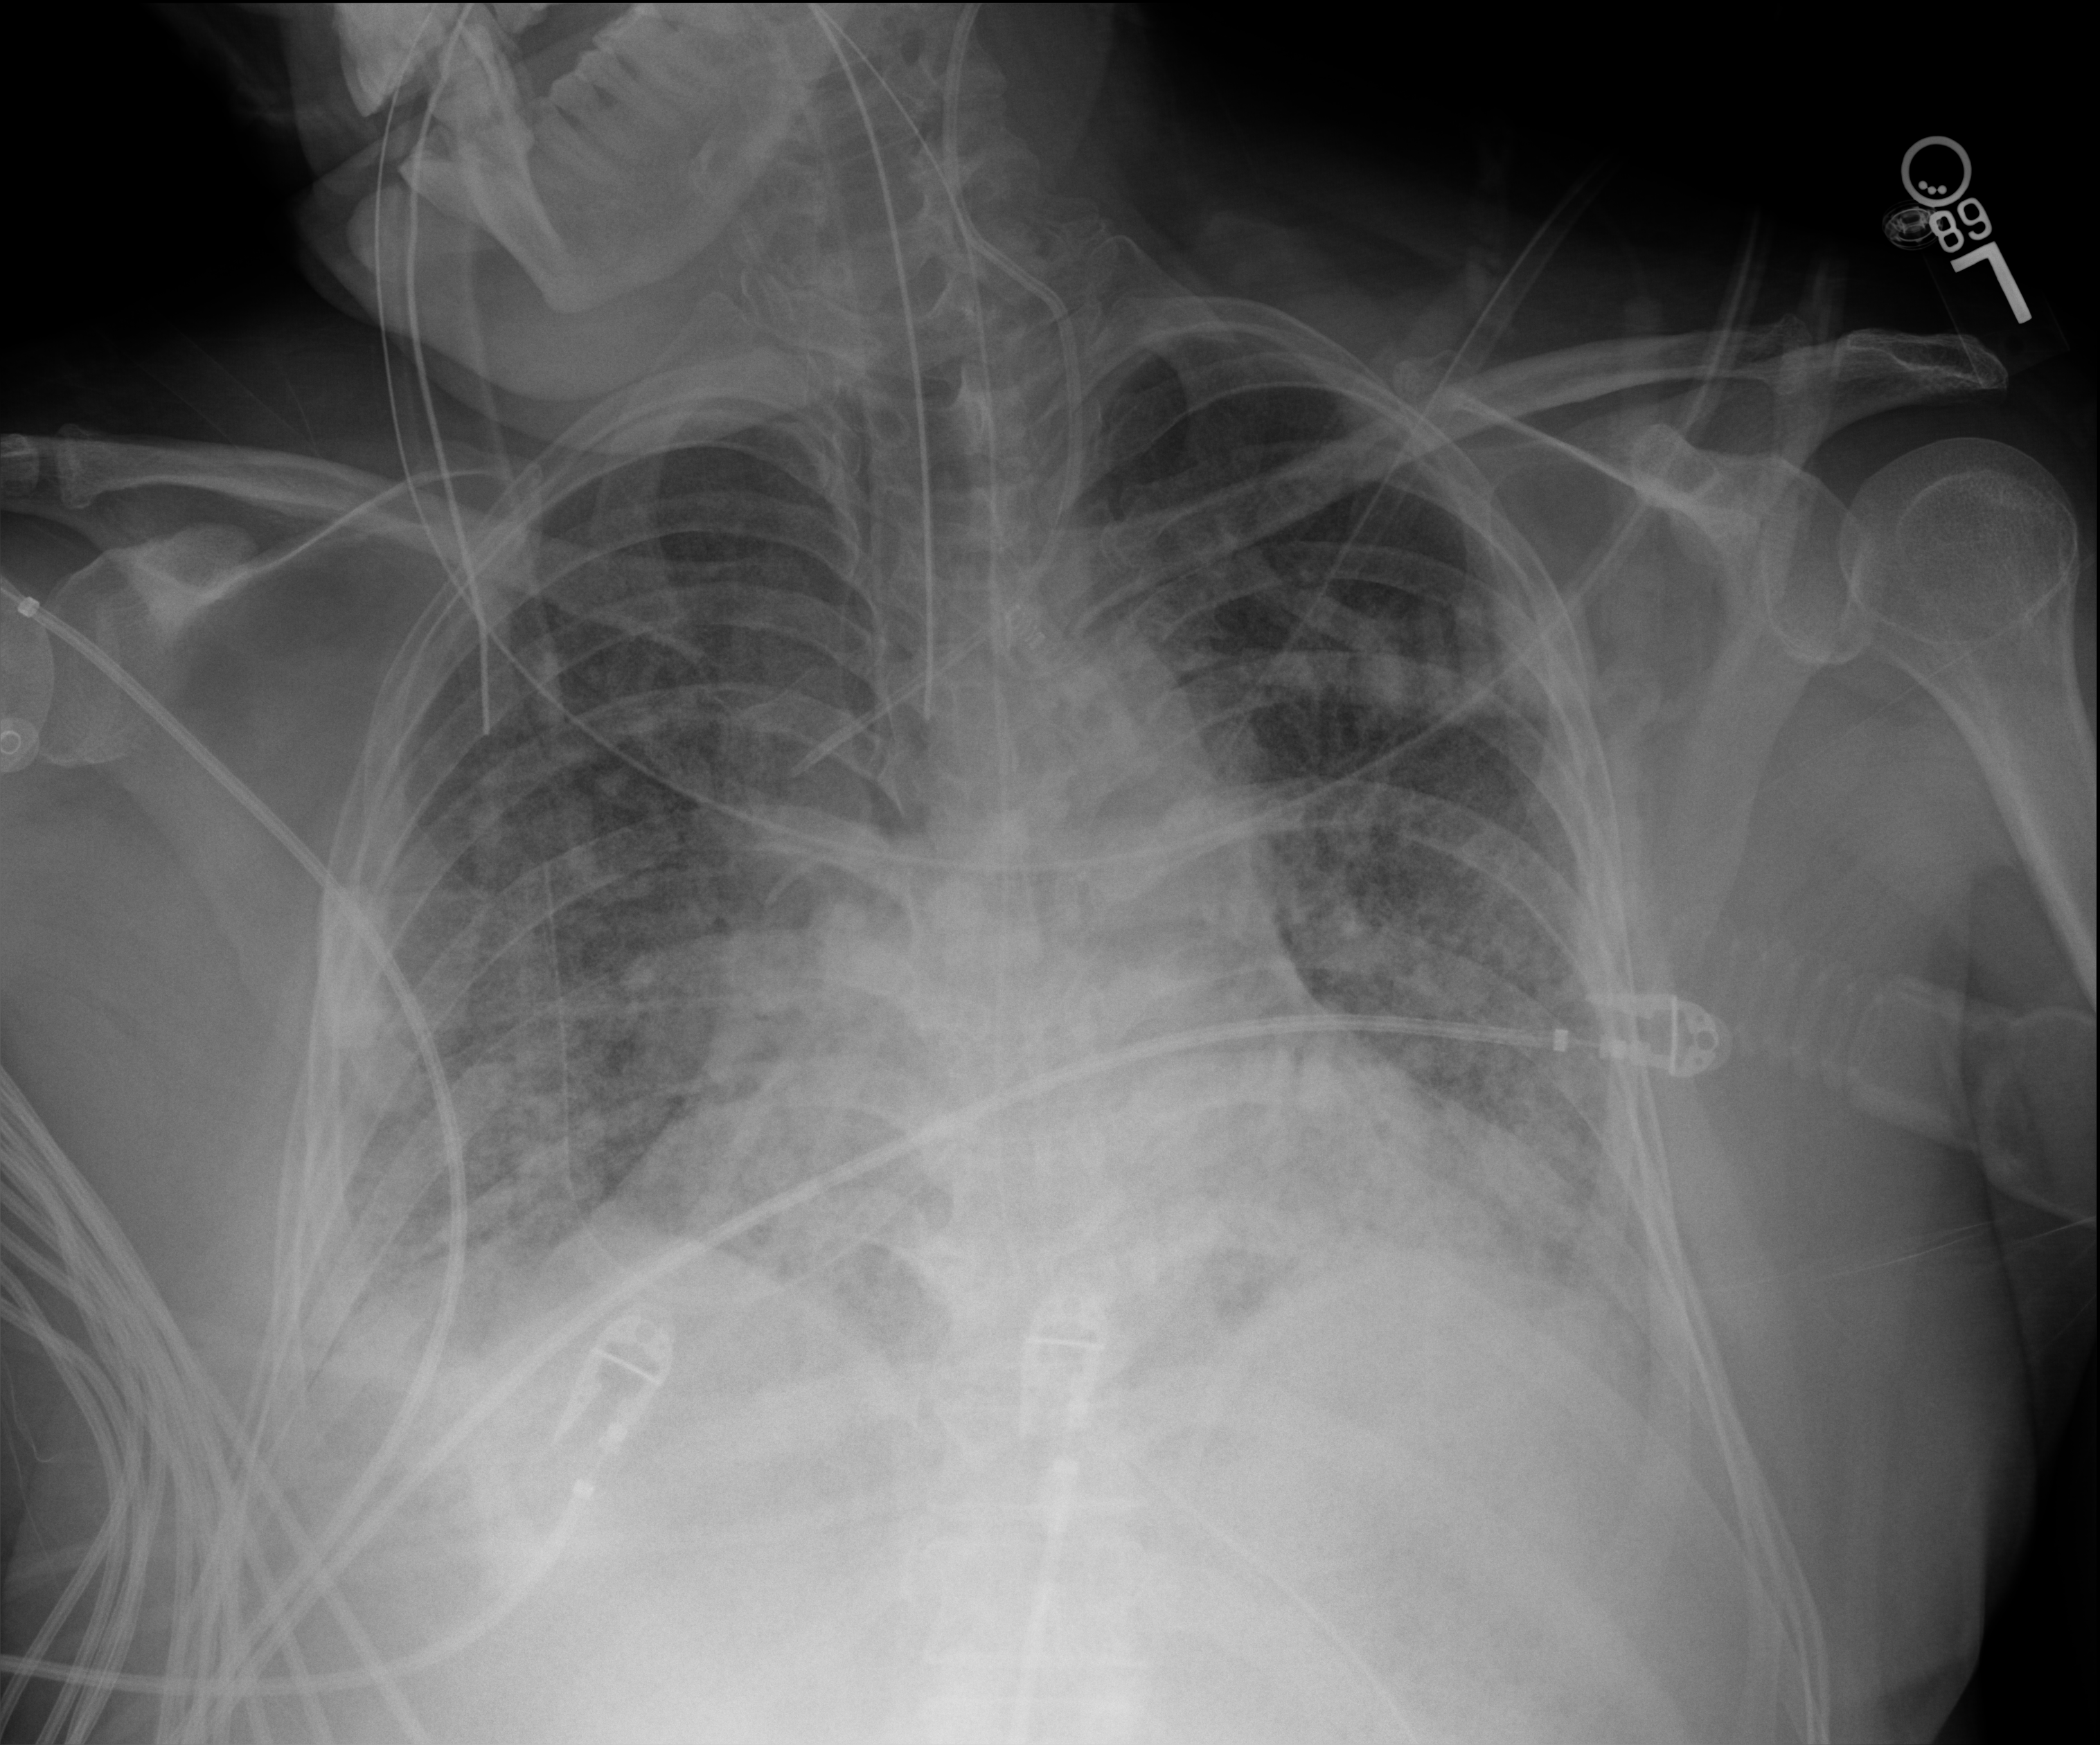
Bedside chest radiograph (digital radiography). Patient hospitalised with COVID-19, aged 18–59 years.
Admission-level facts for this patient (not findings on this image; timing relative to this image not recorded): length of hospital stay: 48 days; mechanically ventilated during this hospital stay: yes; chronic kidney disease (admission record): no.